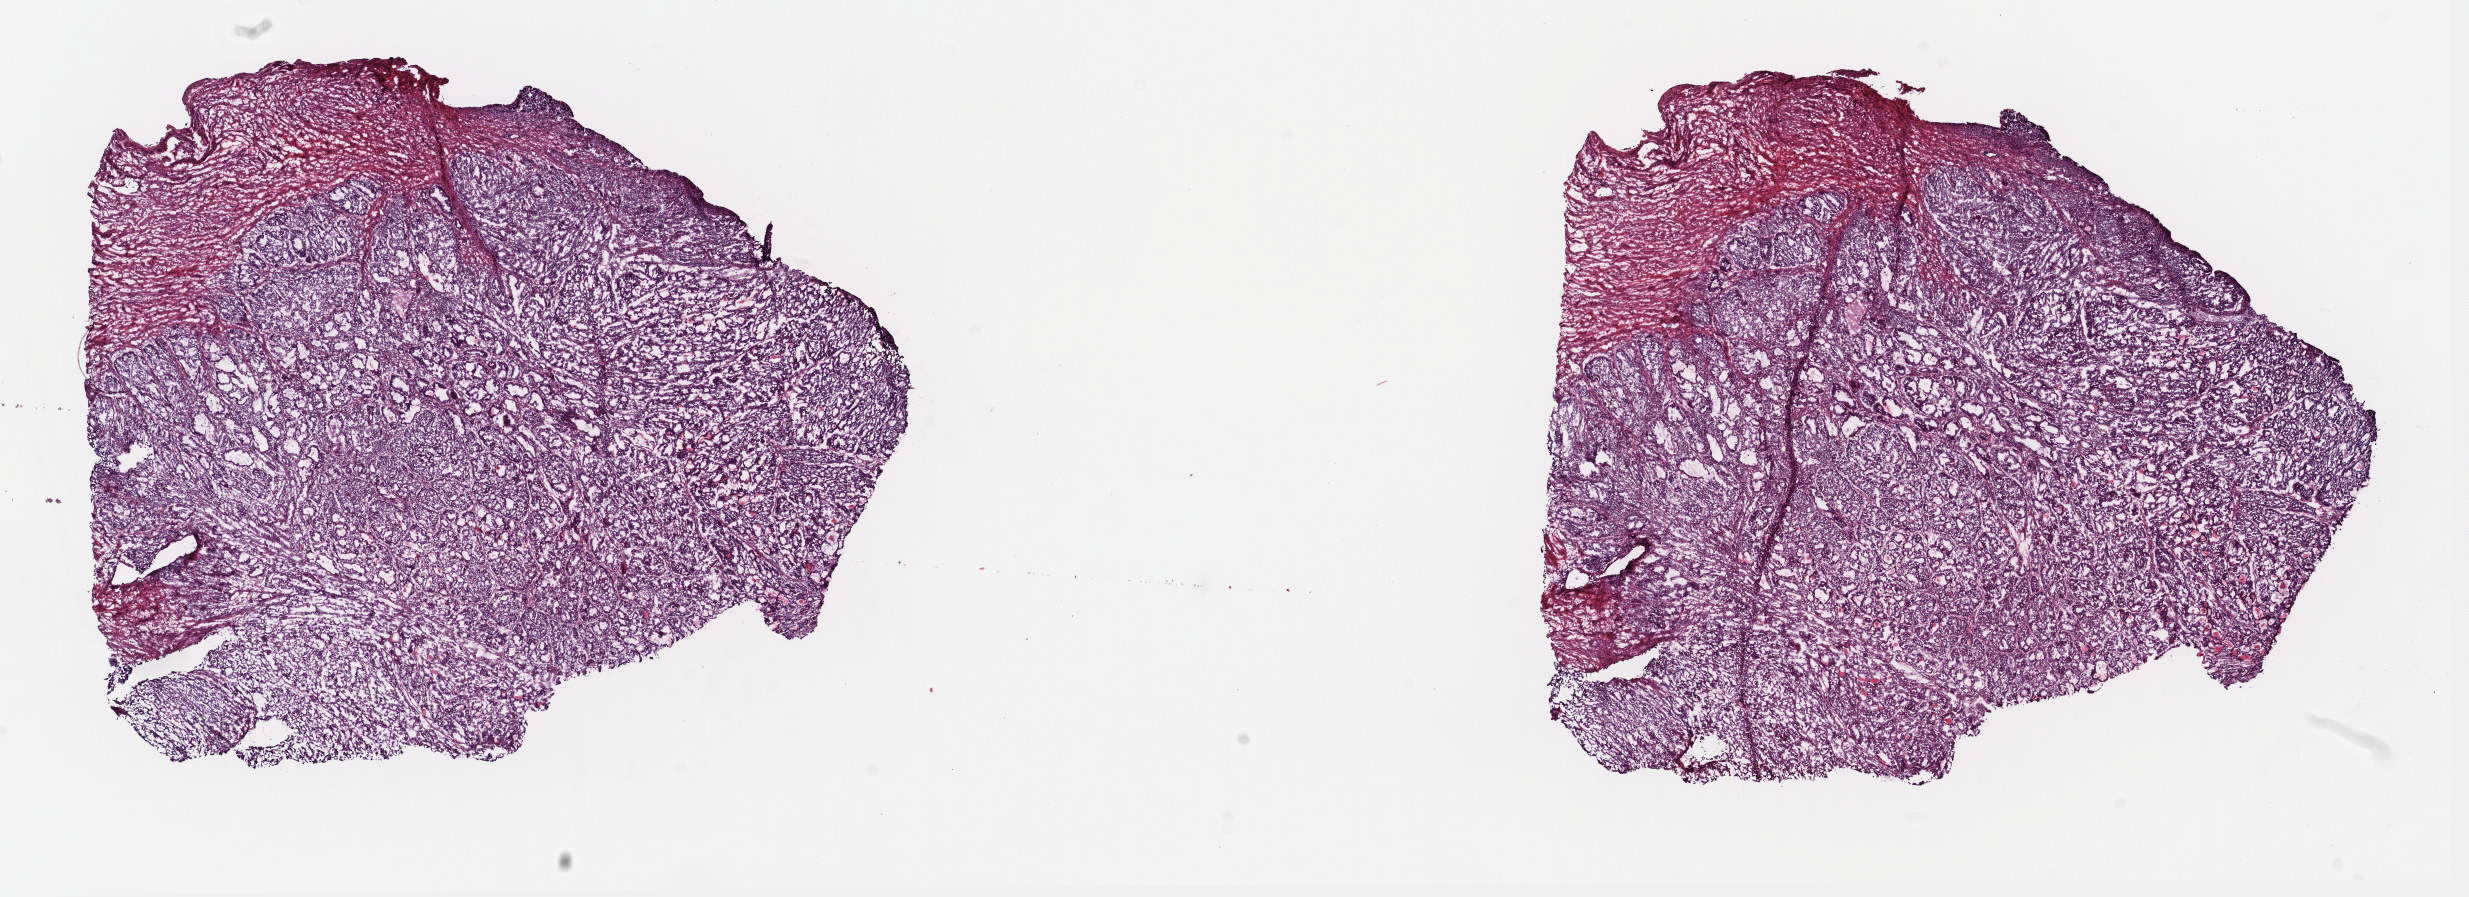
Digitized Hematoxylin and eosin (H&E) stained tissue section (whole slide), whole scanned area (about 19.5 x 7.1 mm, acquisition: 40x scan) shown as a low-resolution overview. Frozen section from the top of the tissue portion. Primary tumour sample from the uterus. Female patient; age at initial diagnosis 73 years. Histologic grade: G2 (moderately differentiated). Slide review estimates, as recorded: tumour cells 50%, tumour nuclei 60%, normal cells 20%, stromal cells 20%, necrosis 10%. Infiltration values recorded for this section: lymphocyte infiltration 20%, monocyte infiltration 0%, neutrophil infiltration 10%.
• diagnosis: Endometrioid adenocarcinoma, NOS (endometrium)
• FIGO stage: IA